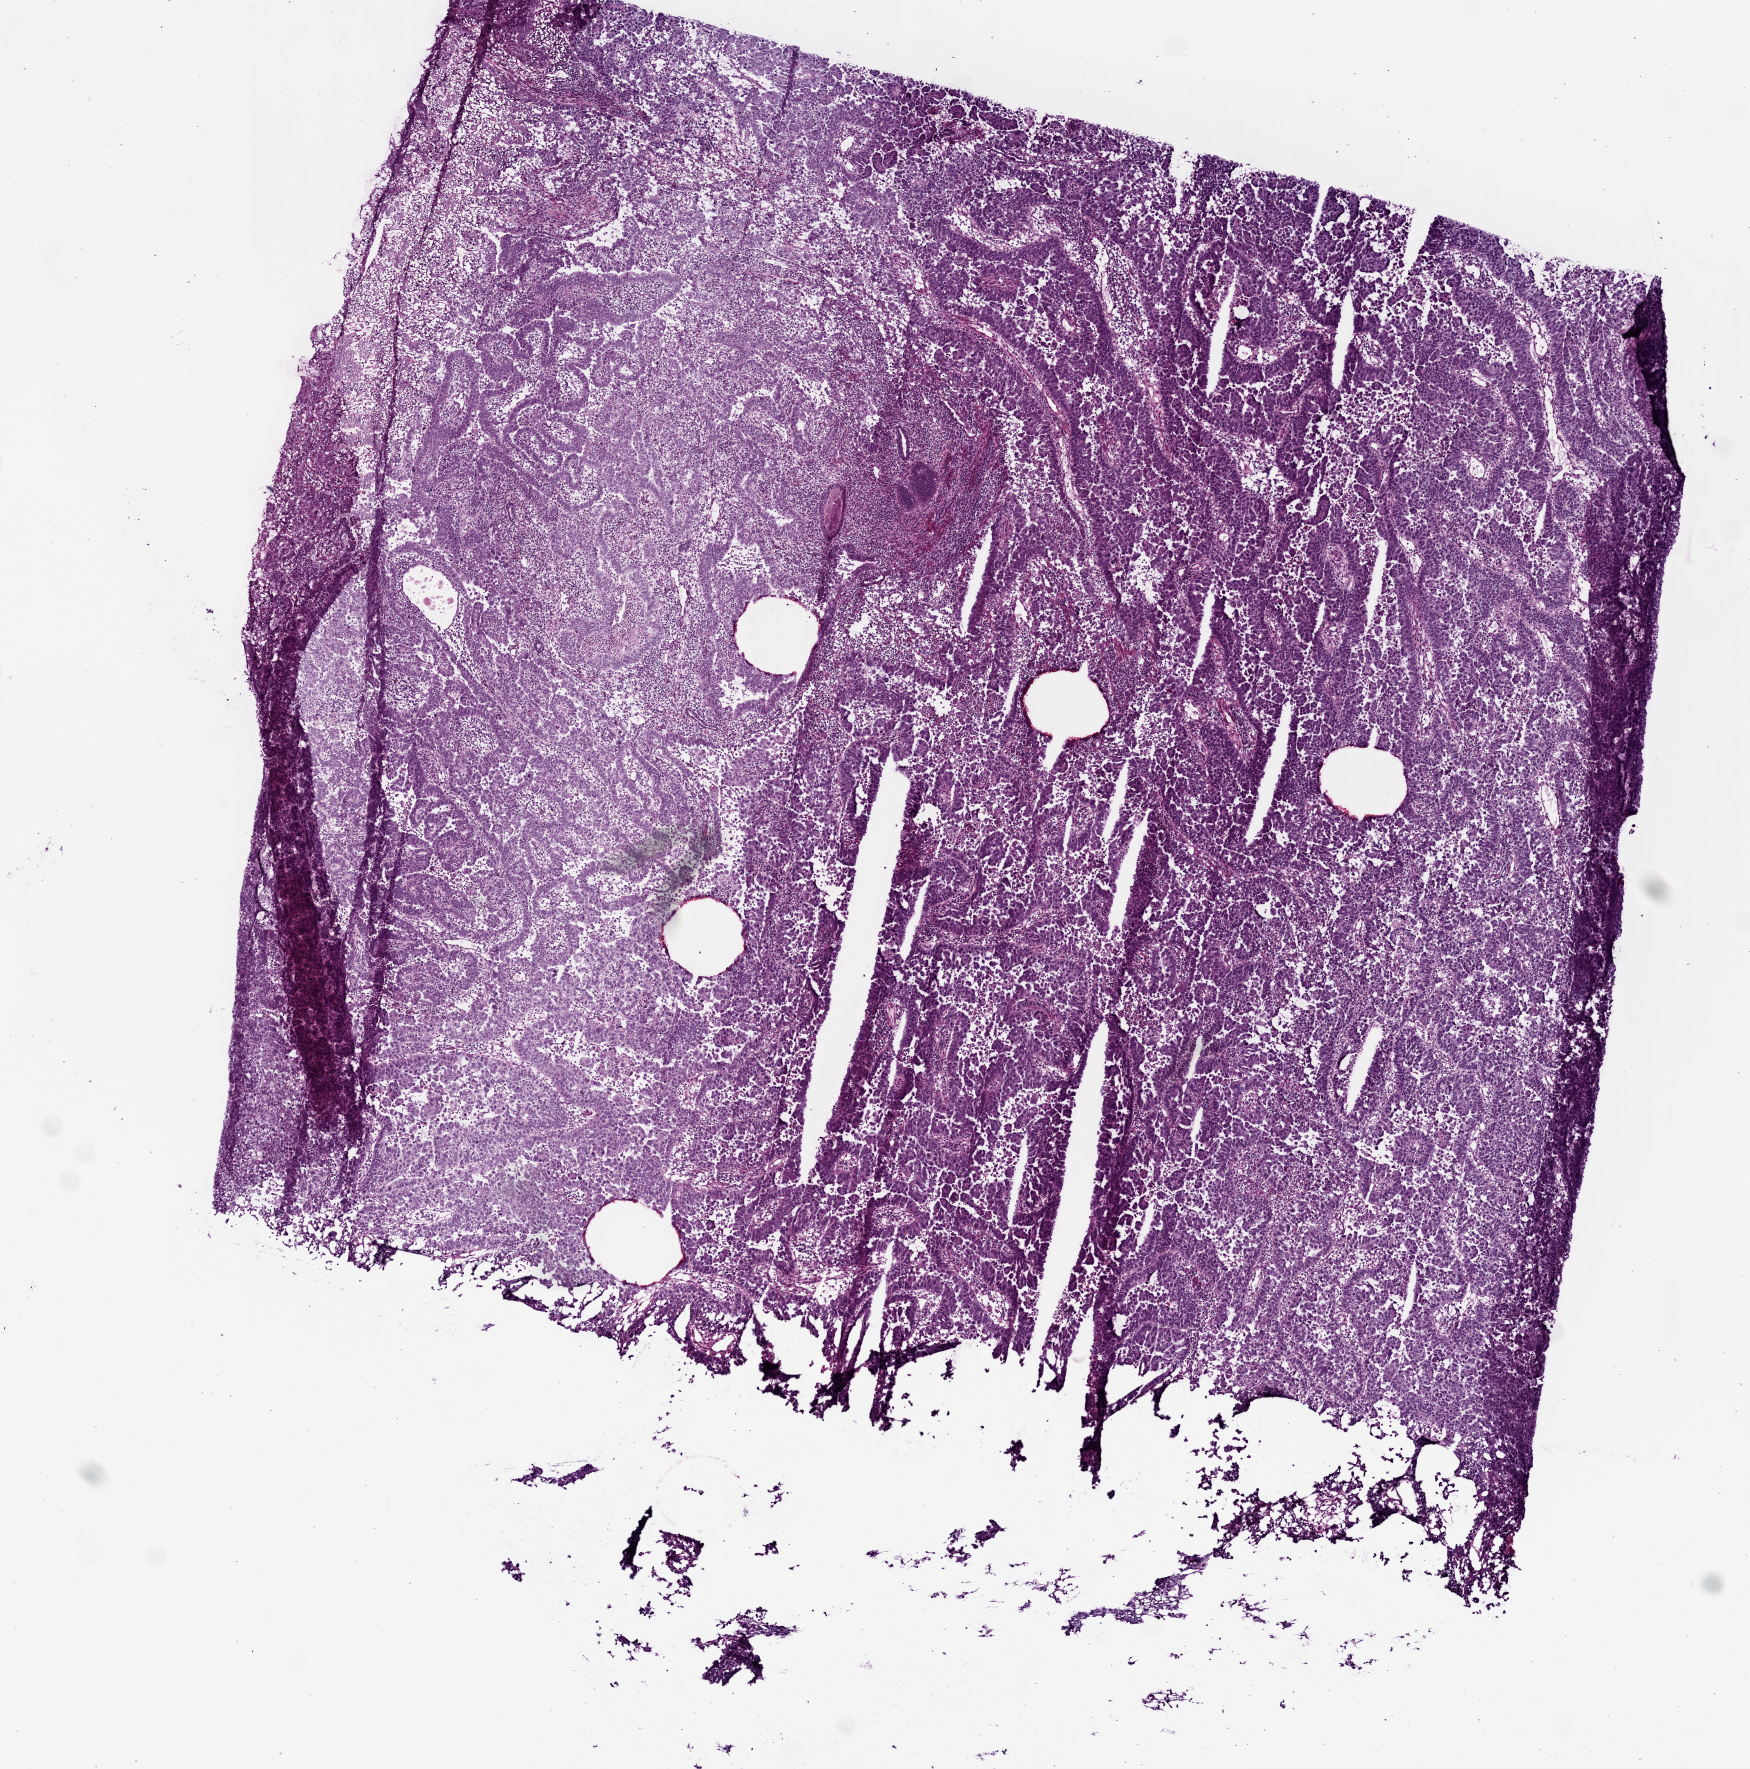
H&E-stained whole-slide image, a low-resolution overview of the entire scanned area, about 7.0 x 7.1 mm (from a 20x scan). Frozen section from the top of the tissue portion. Uterus, primary tumour sample. Female patient; age at initial diagnosis 57 years. Histologic grade: G3 (poorly differentiated). Pathologist review of this section (percent, as recorded): tumour cells 95%, tumour nuclei 60%, normal cells 0%, stromal cells 5%, necrosis 0%. Inflammatory infiltration, as recorded: lymphocyte infiltration 0%, monocyte infiltration 0%, neutrophil infiltration 0%.
Pathologic diagnosis: Serous cystadenocarcinoma, NOS (endometrium). FIGO stage: IIIA.